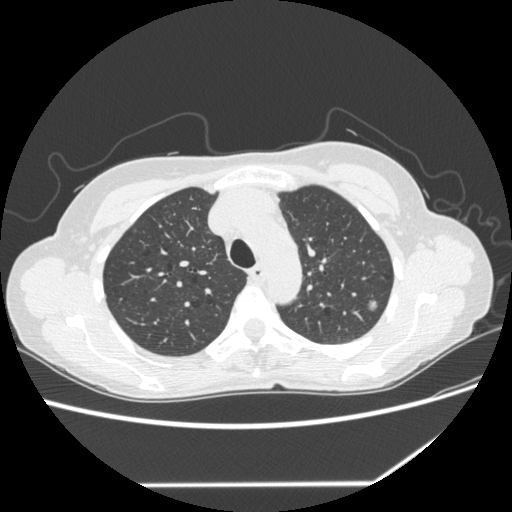
Low-dose screening chest CT, one axial slice. Reconstruction kernel STANDARD. Lung window (W 1500 / L -600 HU). 512 × 512 image matrix, field of view 360 × 360 mm.
Annotated regions visible in this slice (expert manual segmentation):
- lesion 1 (tumor, upper lobe of left lung): bounding box [x1, y1, x2, y2] px = [369, 301, 377, 310]